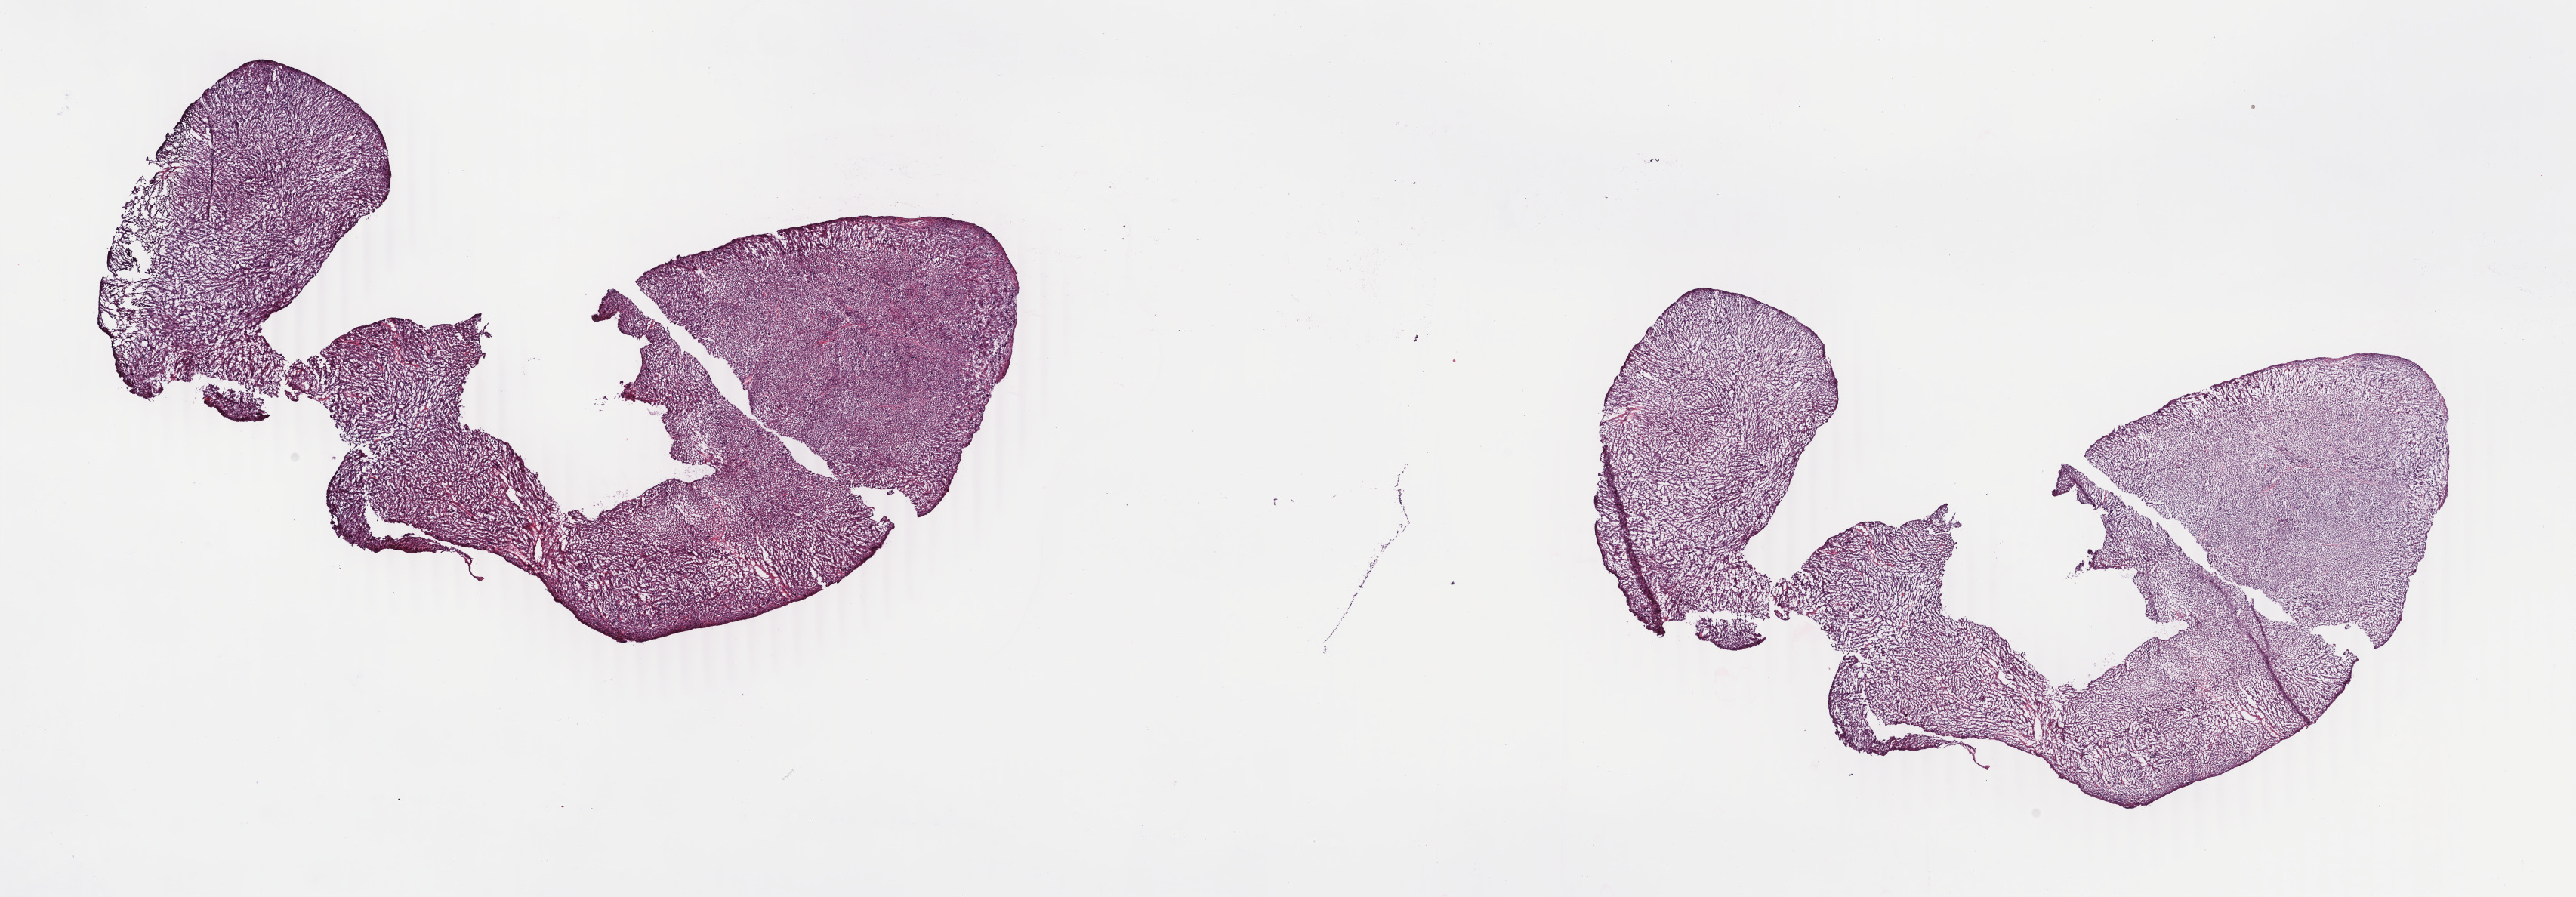
H&E-stained whole-slide image, low-resolution overview of the scanned area, about 27.1 x 9.4 mm (slide scanned at 40x), frozen section from the top of the tissue portion, primary tumour sample from the corpus uteri. Patient: female, age at initial diagnosis 35 years. Pathologist review of this section (percent, as recorded): tumour cells 90%, tumour nuclei 90%, normal cells 0%, stromal cells 10%, necrosis 0%. Inflammatory infiltration, as recorded: lymphocyte infiltration 0%, monocyte infiltration 0%, neutrophil infiltration 0%.
Pathologic diagnosis: Leiomyosarcoma, NOS.